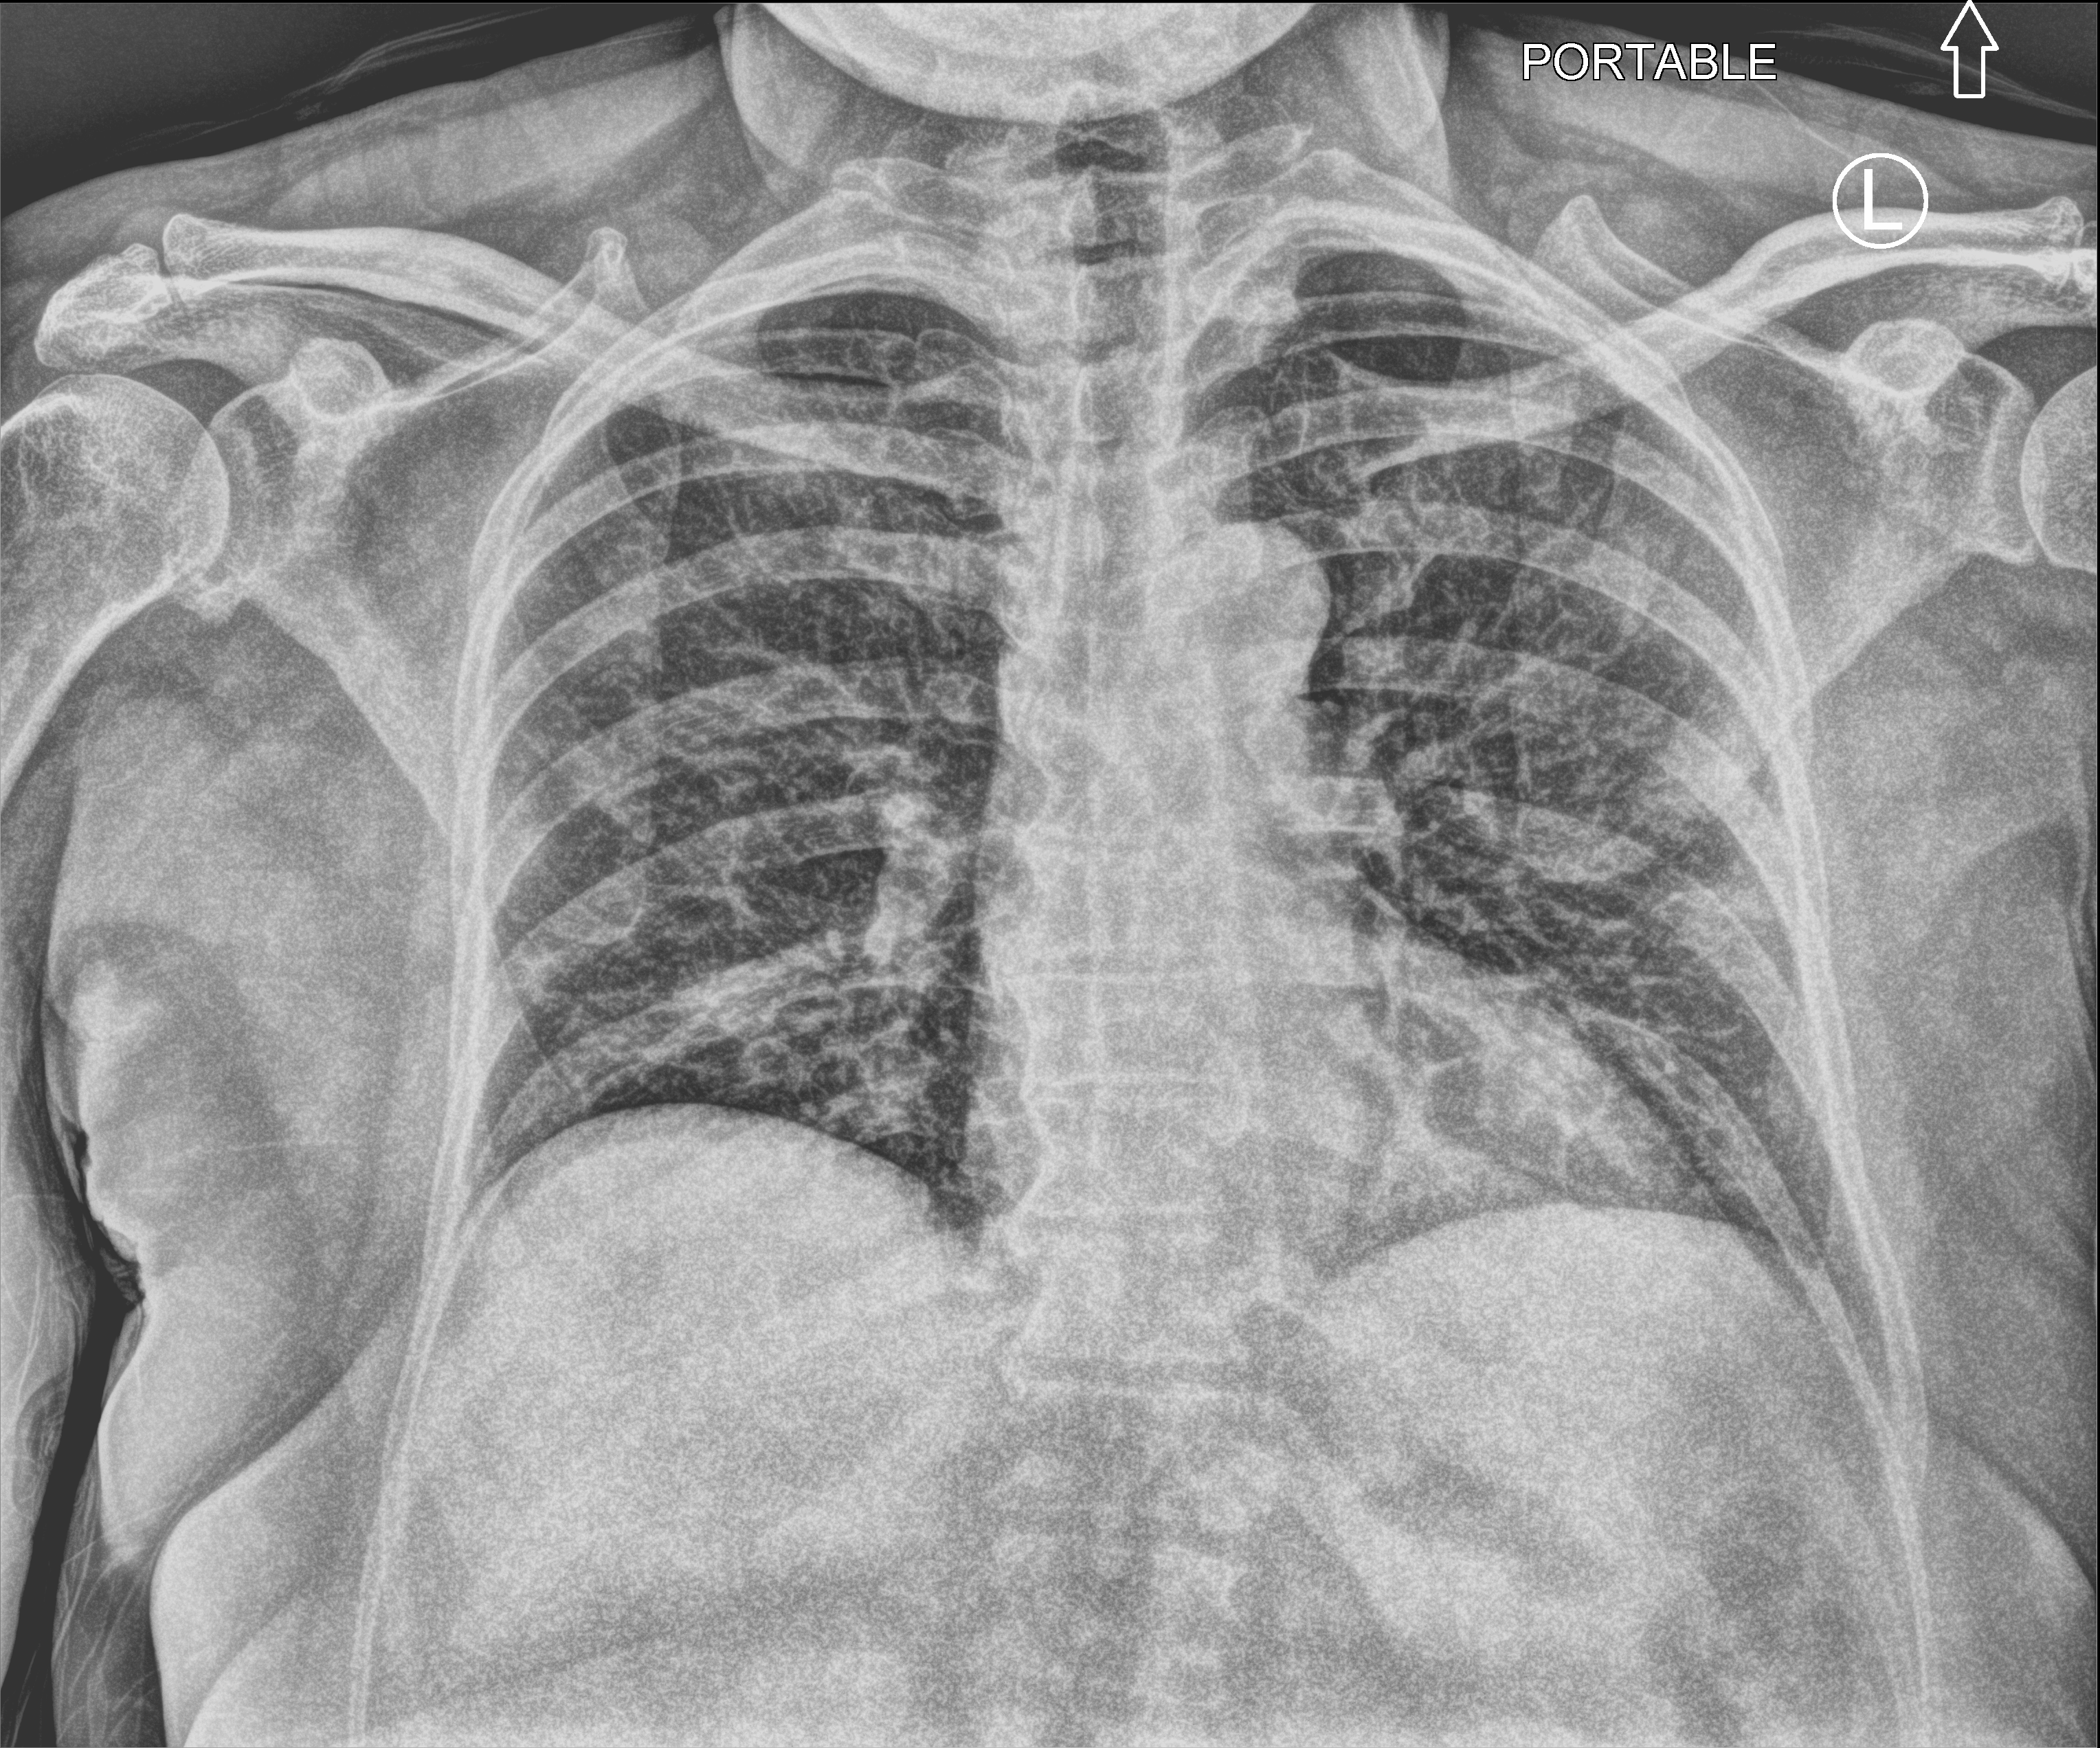
Bedside chest radiograph (computed radiography); anteroposterior (AP) projection. Female patient hospitalised with COVID-19, age 18–59 years.
From the hospital-stay record, not from the radiograph (when in the stay this image was taken is not recorded):
- admitted to intensive care during this hospital stay: no
- mechanically ventilated during this hospital stay: no